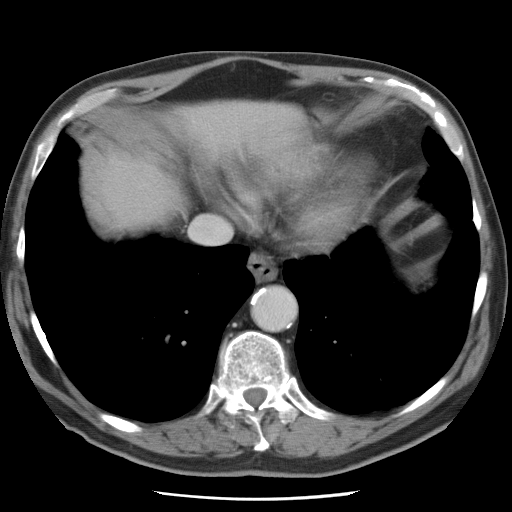
Contrast-enhanced abdominal CT, one axial slice; soft-tissue window (W 400 / L 40 HU); 5 mm slice thickness; 512 × 512 image matrix. Male patient, age 75 years. Case-level facts recorded for this patient, not image findings: diagnosis: colorectal cancer liver metastases, imaged before liver resection; multiple liver metastases: yes; largest metastasis: 2.4 cm; disease in both lobes: yes.
Outlined on this slice (manually delineated by an expert):
- liver: bounding box <97,102,289,228> (left, top, right, bottom; pixels)
- planned liver remnant (the part of the liver to remain after resection): <99,171,162,226>